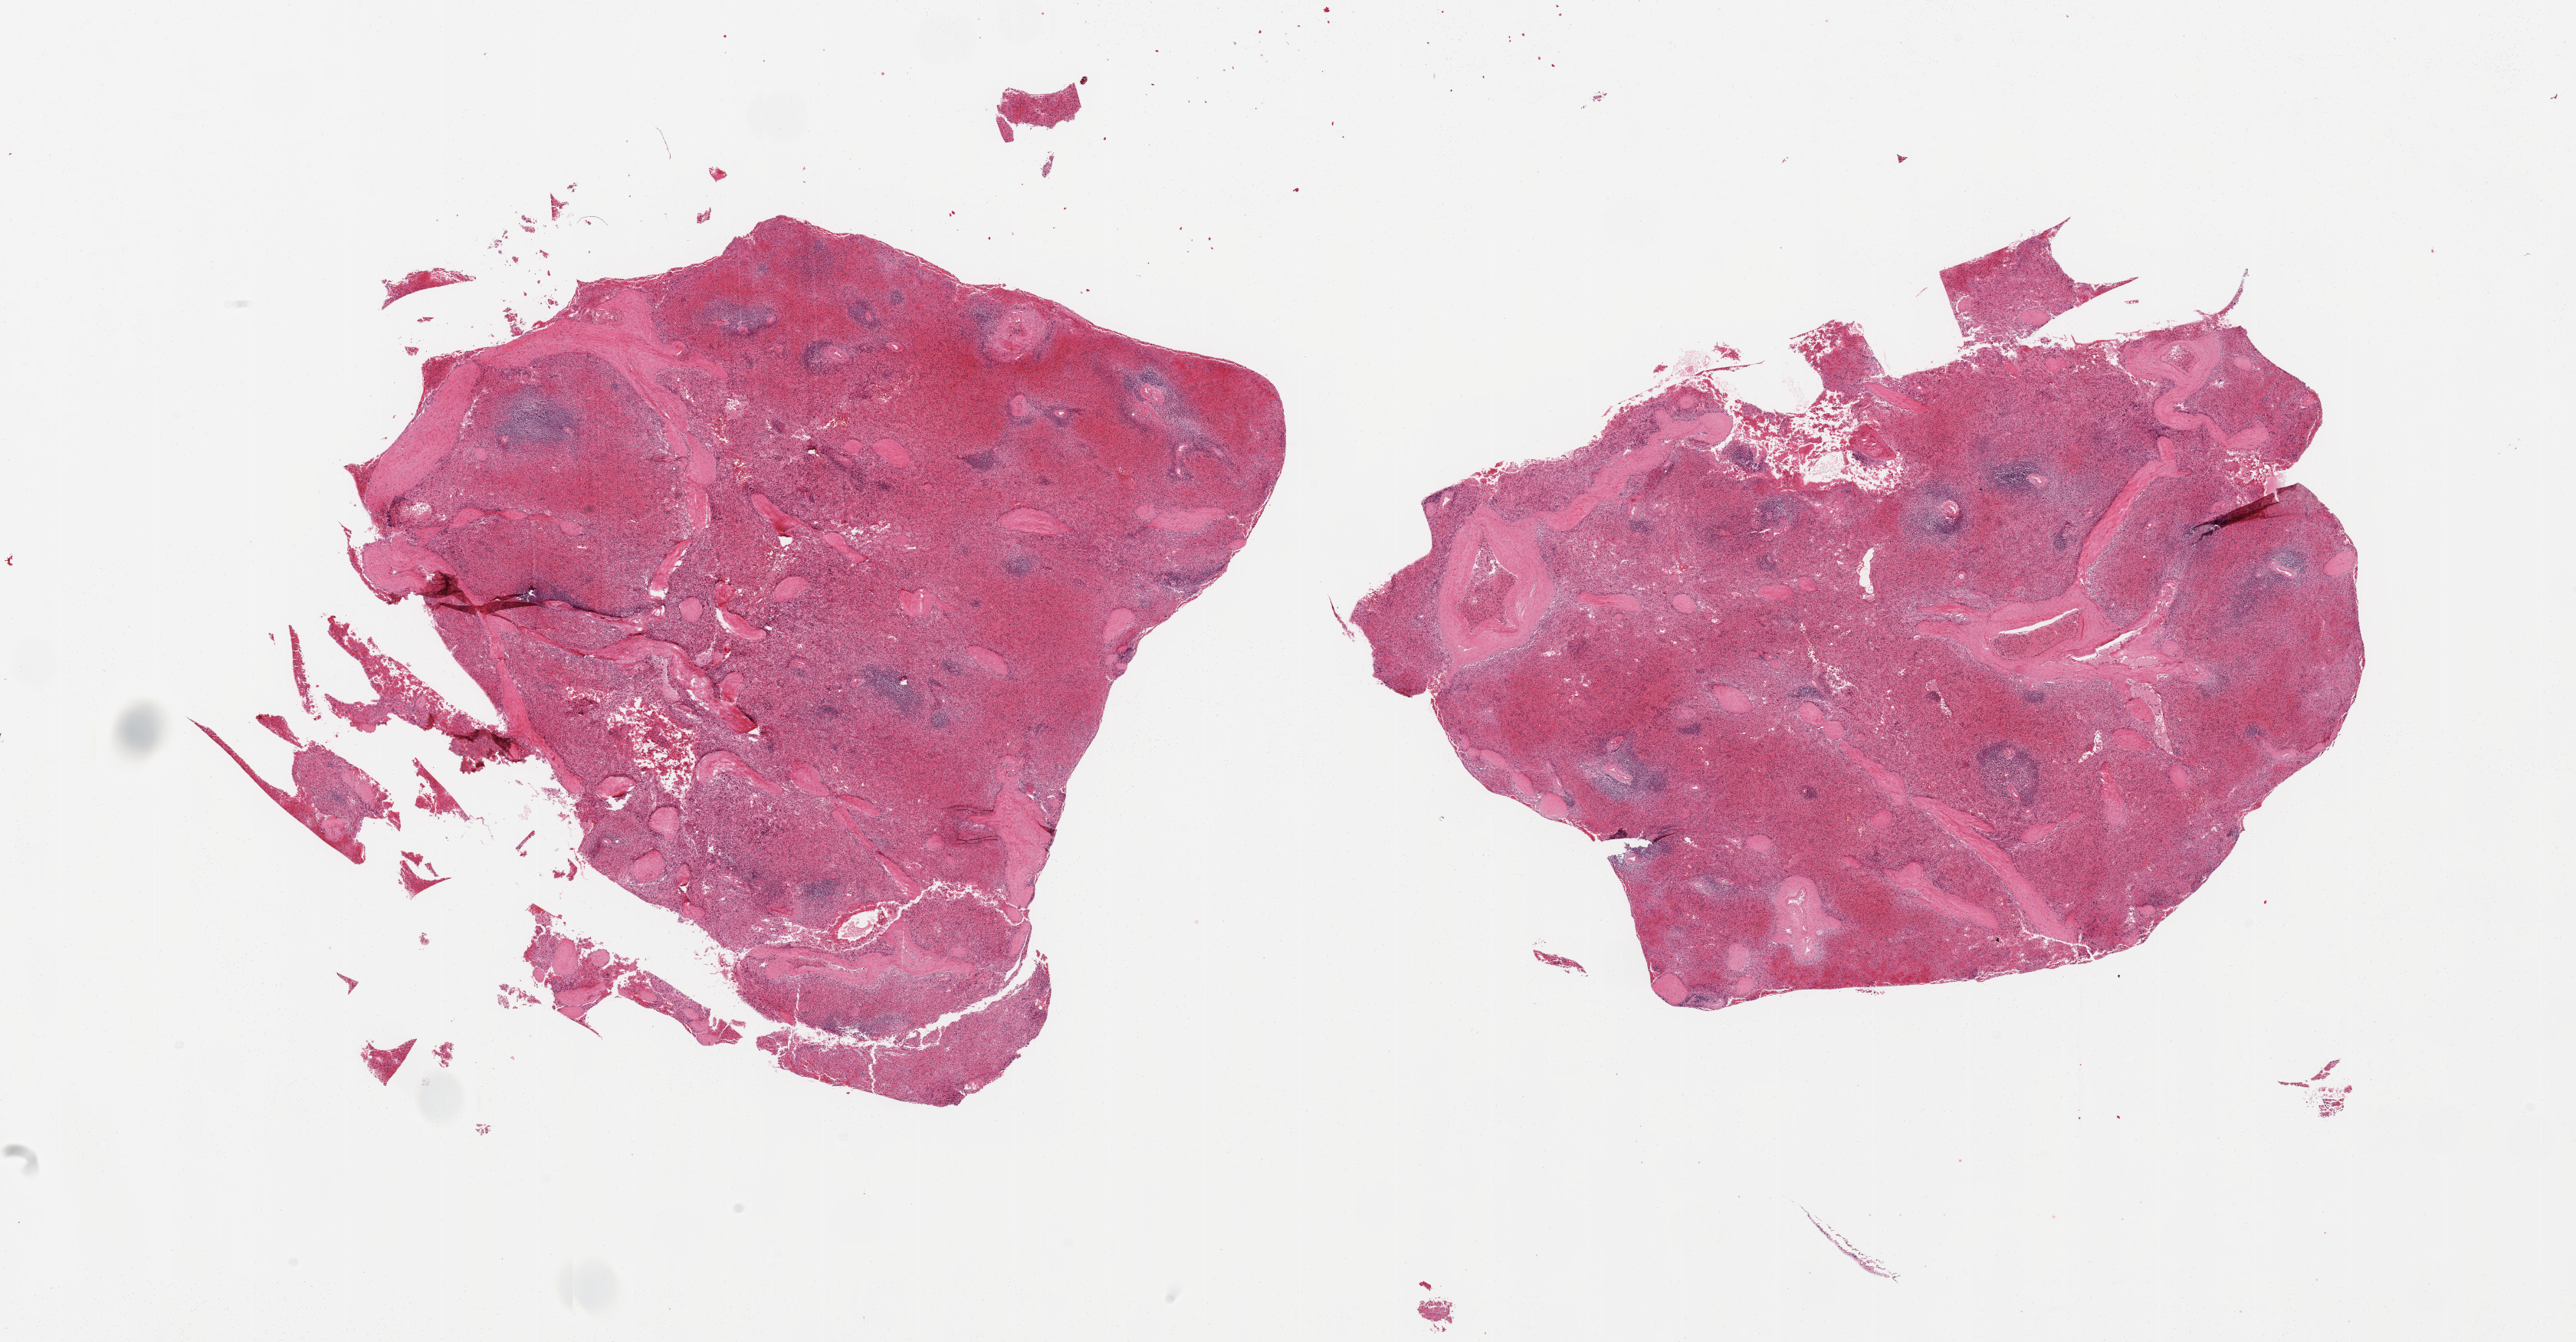
Whole-slide image, haematoxylin and eosin stain, low-resolution overview of the scanned area, about 26.6 x 13.8 mm (from a 20x scan), PAXgene-fixed, paraffin-embedded tissue, sampled site (target tissue): spleen, donor tissue sample. Donor sex: male.
Pathologist's review note for this sample: 2 pieces, moderate congestion.